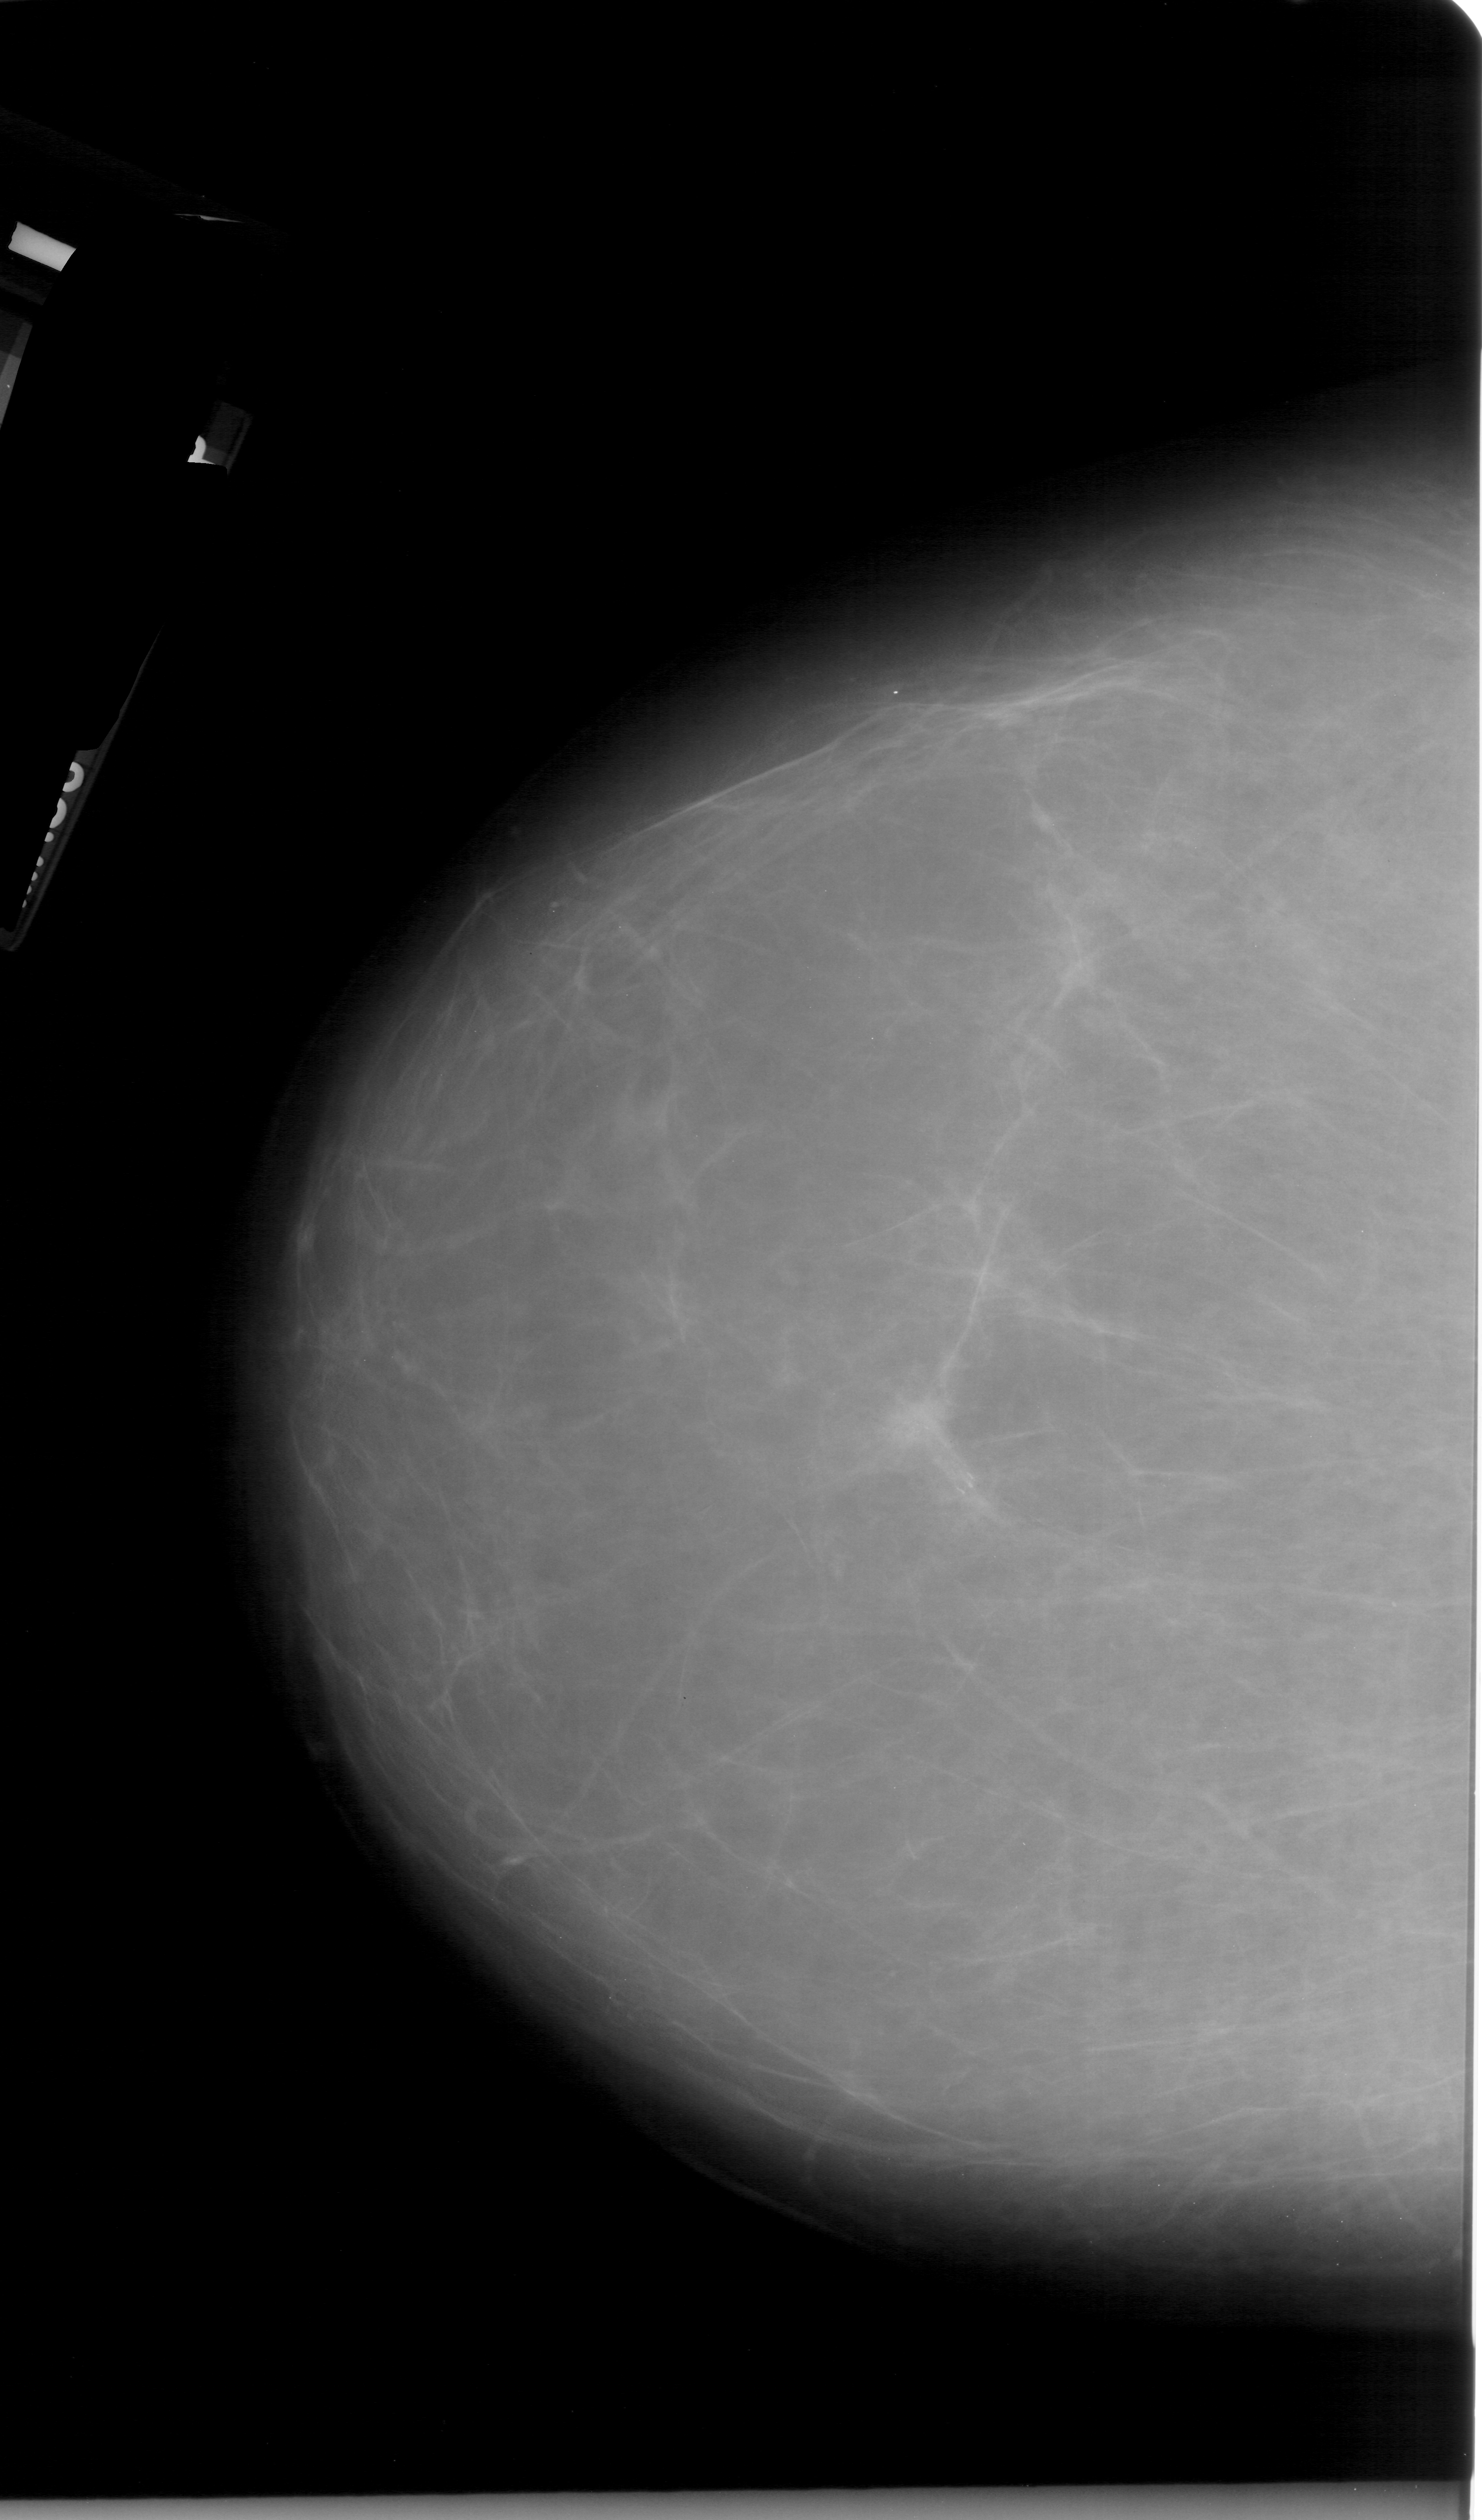
Digitized screen-film mammogram; left breast; CC view; BI-RADS breast density category 1 (scale 1–4); 1482 × 2520 image matrix.
Marked abnormalities (boxes around the expert regions of interest):
- calcifications, morphology fine linear branching, distribution clustered; BI-RADS assessment category 4; pathology (as recorded): malignant: box from (x=869, y=1392) to (x=1001, y=1538) px